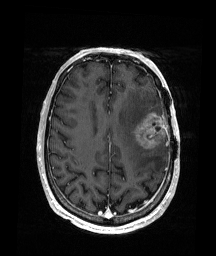
Brain MRI from a brain-tumour surgery series, one axial slice; position 67 of 176 along the scan axis; T1-weighted post-contrast; 1 mm slice thickness; 216 × 256 image matrix. From the clinical record (not read from this slice): histopathology: Glioblastoma; WHO grade: 4; IDH mutation: no.
Outlined on this slice (expert manual segmentation):
- tumour: bounding box (x1, y1, x2, y2) in pixels: (132, 112, 167, 149)